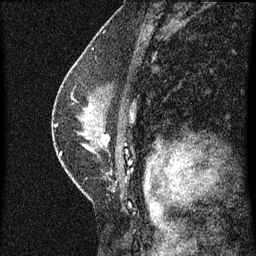
Breast MRI (dynamic contrast-enhanced), one sagittal slice; slice 40 of 60 in the series (ordered by position); dynamic contrast-enhanced series, image 2 of 3 at this slice position (ordered by acquisition); 1.5 T; TE 4.2 ms, TR 8 ms; 2 mm slice thickness; 256 × 256 image matrix, field of view 180 × 180 mm. Patient: female, 47 years.
Annotated regions visible in this slice (semi-automatic segmentation, software-assisted and operator-edited):
- analysis volume of interest (the breast-tissue region the enhancement analysis was run in; not a lesion): bounding box (x1, y1, x2, y2) in pixels: (54, 80, 135, 187)
- tumour enhancement mask (voxels above the 70 % enhancement threshold inside the analysis volume of interest): (56, 124, 62, 155)